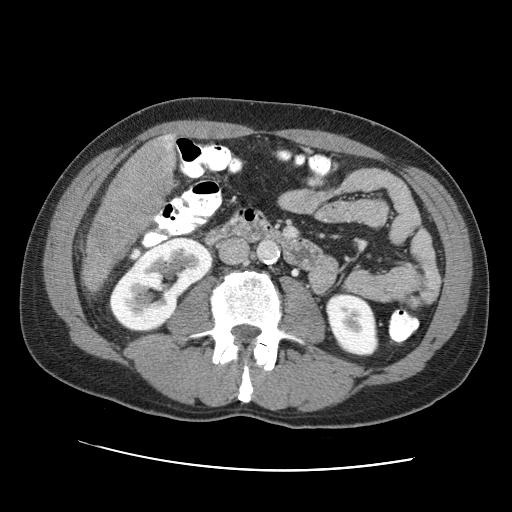
Contrast-enhanced abdominal CT (liver protocol), one axial slice. Position 14 of 95 along the scan axis. Reconstruction kernel STANDARD. One of 2 acquisitions stored at this slice position. Soft-tissue window (W 400 / L 40 HU). 2.5 mm slice thickness. 512 × 512 image matrix, field of view 360 × 360 mm. Case-level facts recorded for this patient, not image findings: diagnosis: hepatocellular carcinoma (patient treated with transarterial chemoembolisation; whether this scan precedes or follows treatment is not stated here); TNM stage (as recorded): Stage-IVA; Child-Pugh class: A; tumour nodularity: multinodular.
Outlined on this slice (semi-automatically segmented with operator editing):
- liver parenchyma outside the tumour (the mass and vessels are separate outlines, so this box may not span the whole liver): box from (x=84, y=134) to (x=174, y=262) px
- mass: (x=80, y=135)–(x=173, y=294)
- liver vessels: (x=168, y=135)–(x=173, y=140)